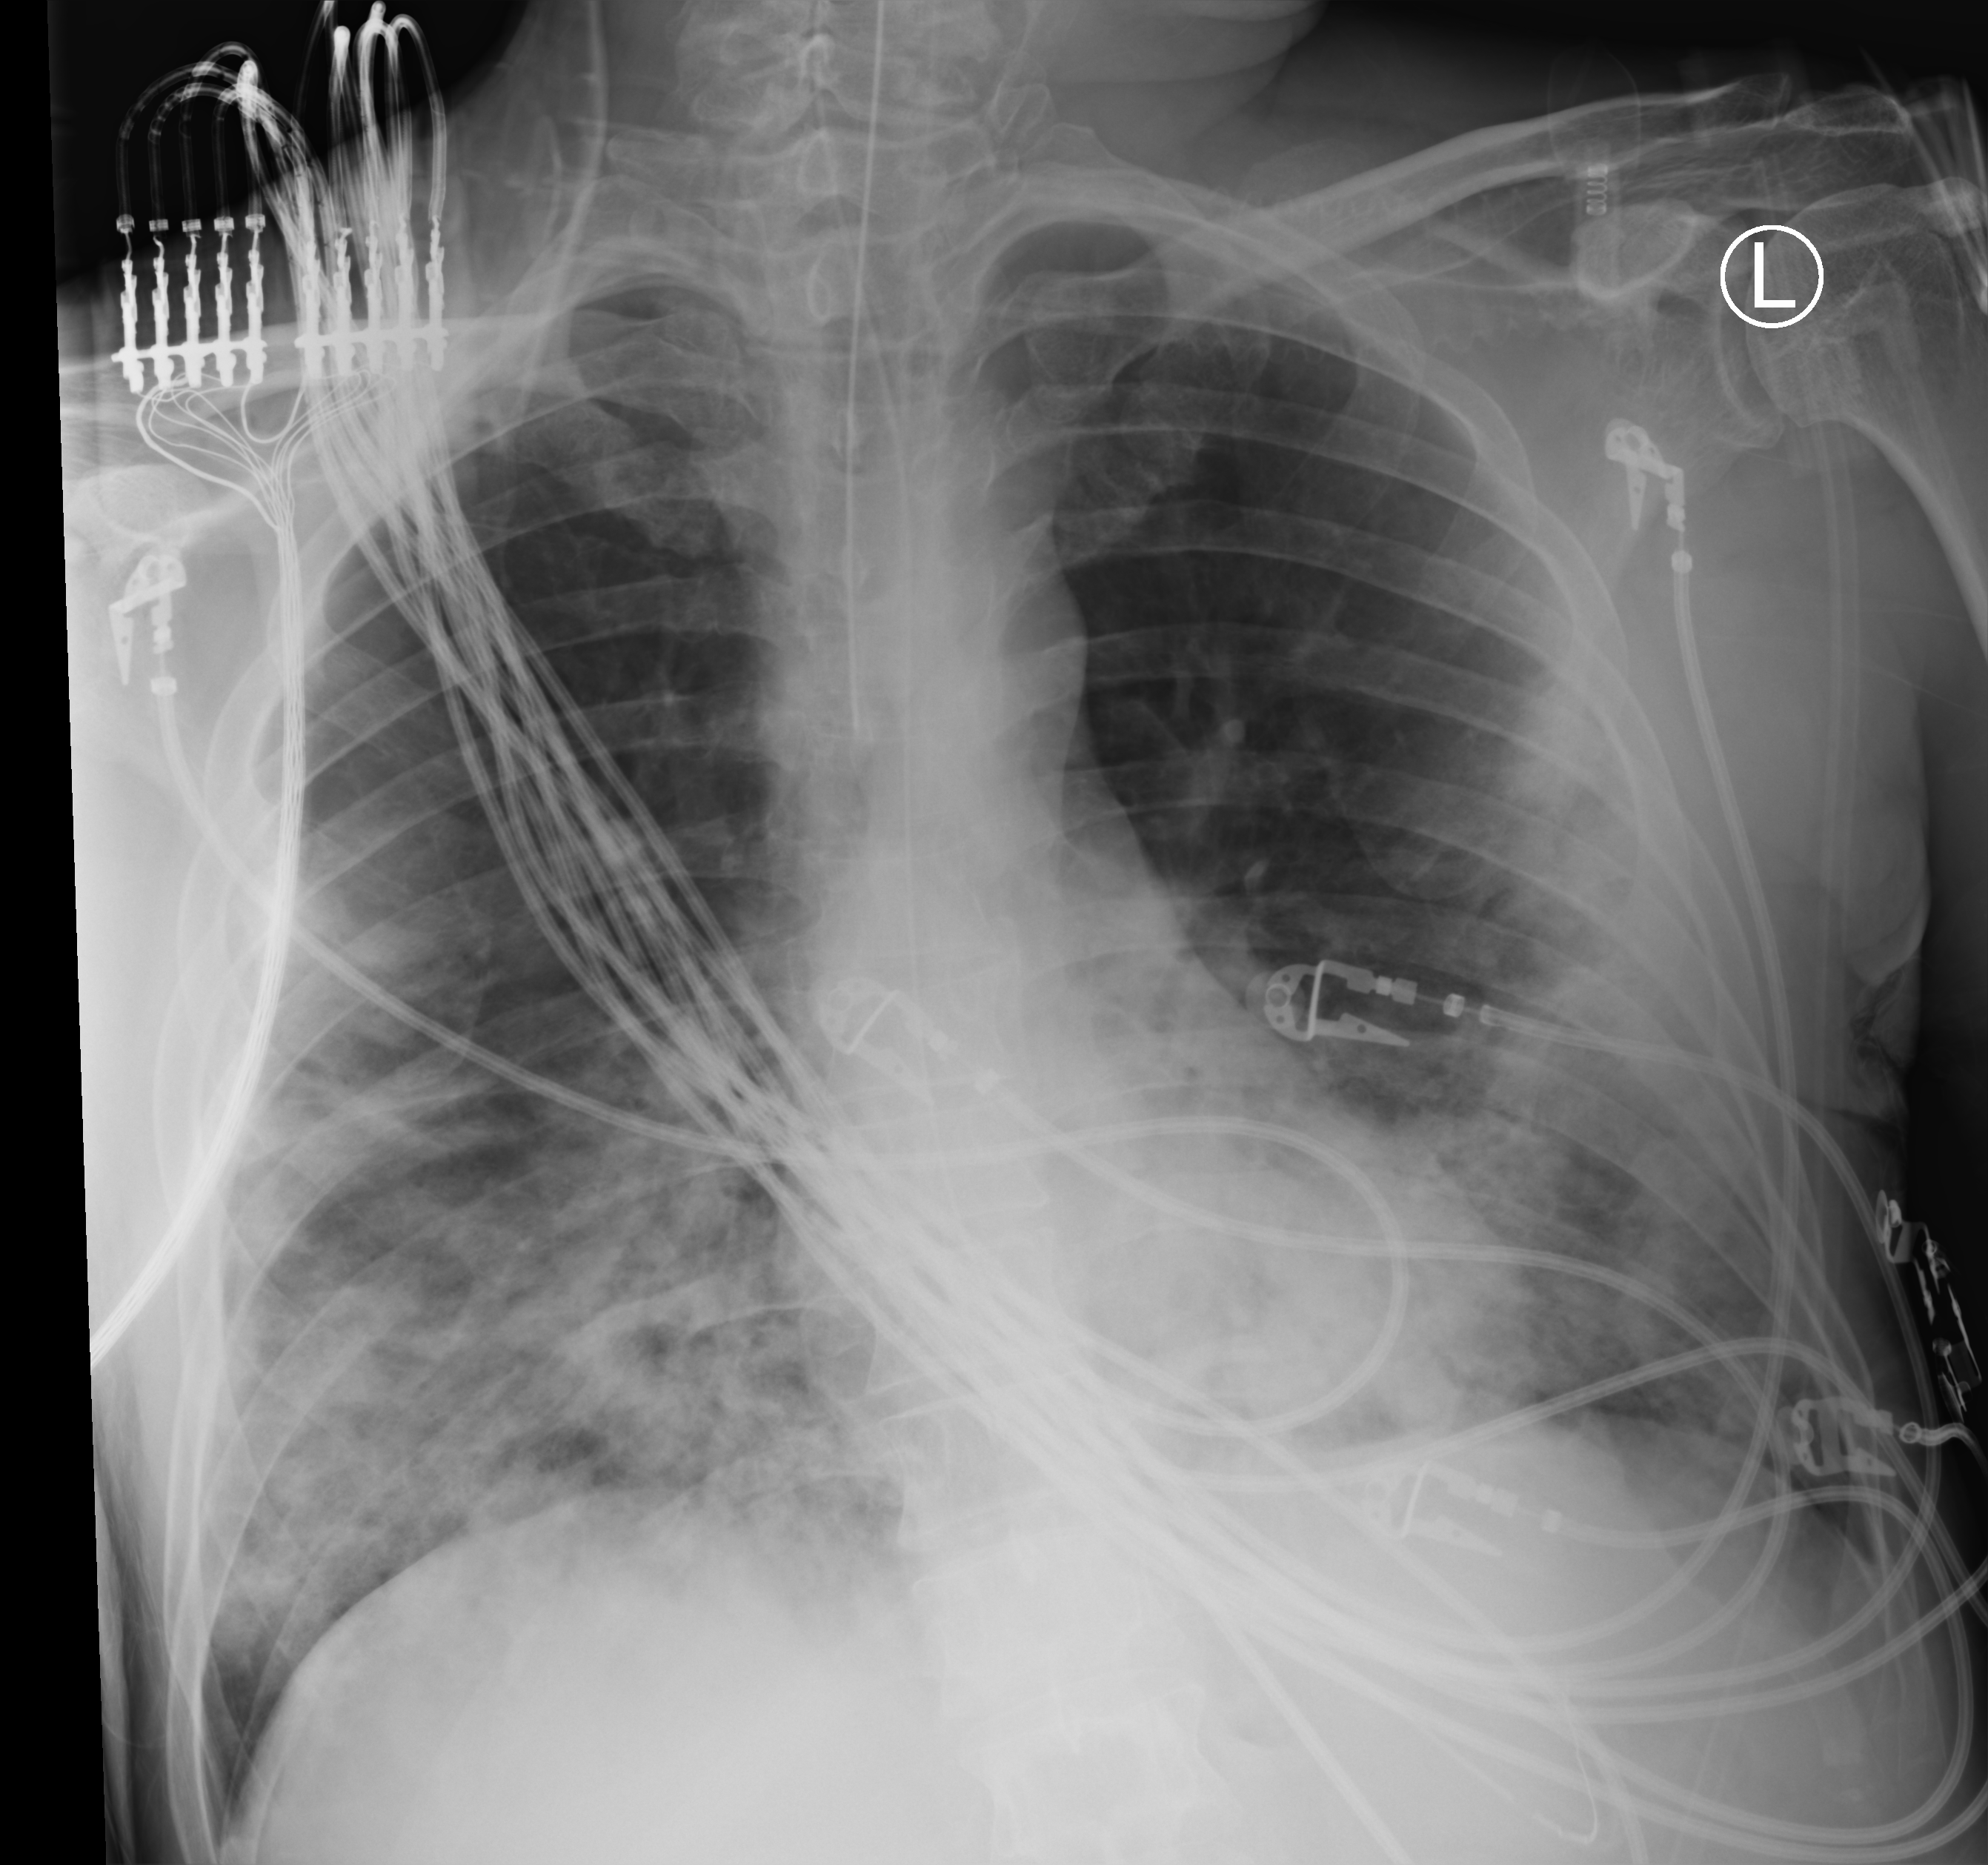
Chest X-ray (portable), anteroposterior (AP) projection. Male patient hospitalised with COVID-19, age 18–59 years.
From the hospital-stay record, not from the radiograph (when in the stay this image was taken is not recorded): mechanically ventilated during this hospital stay: yes.